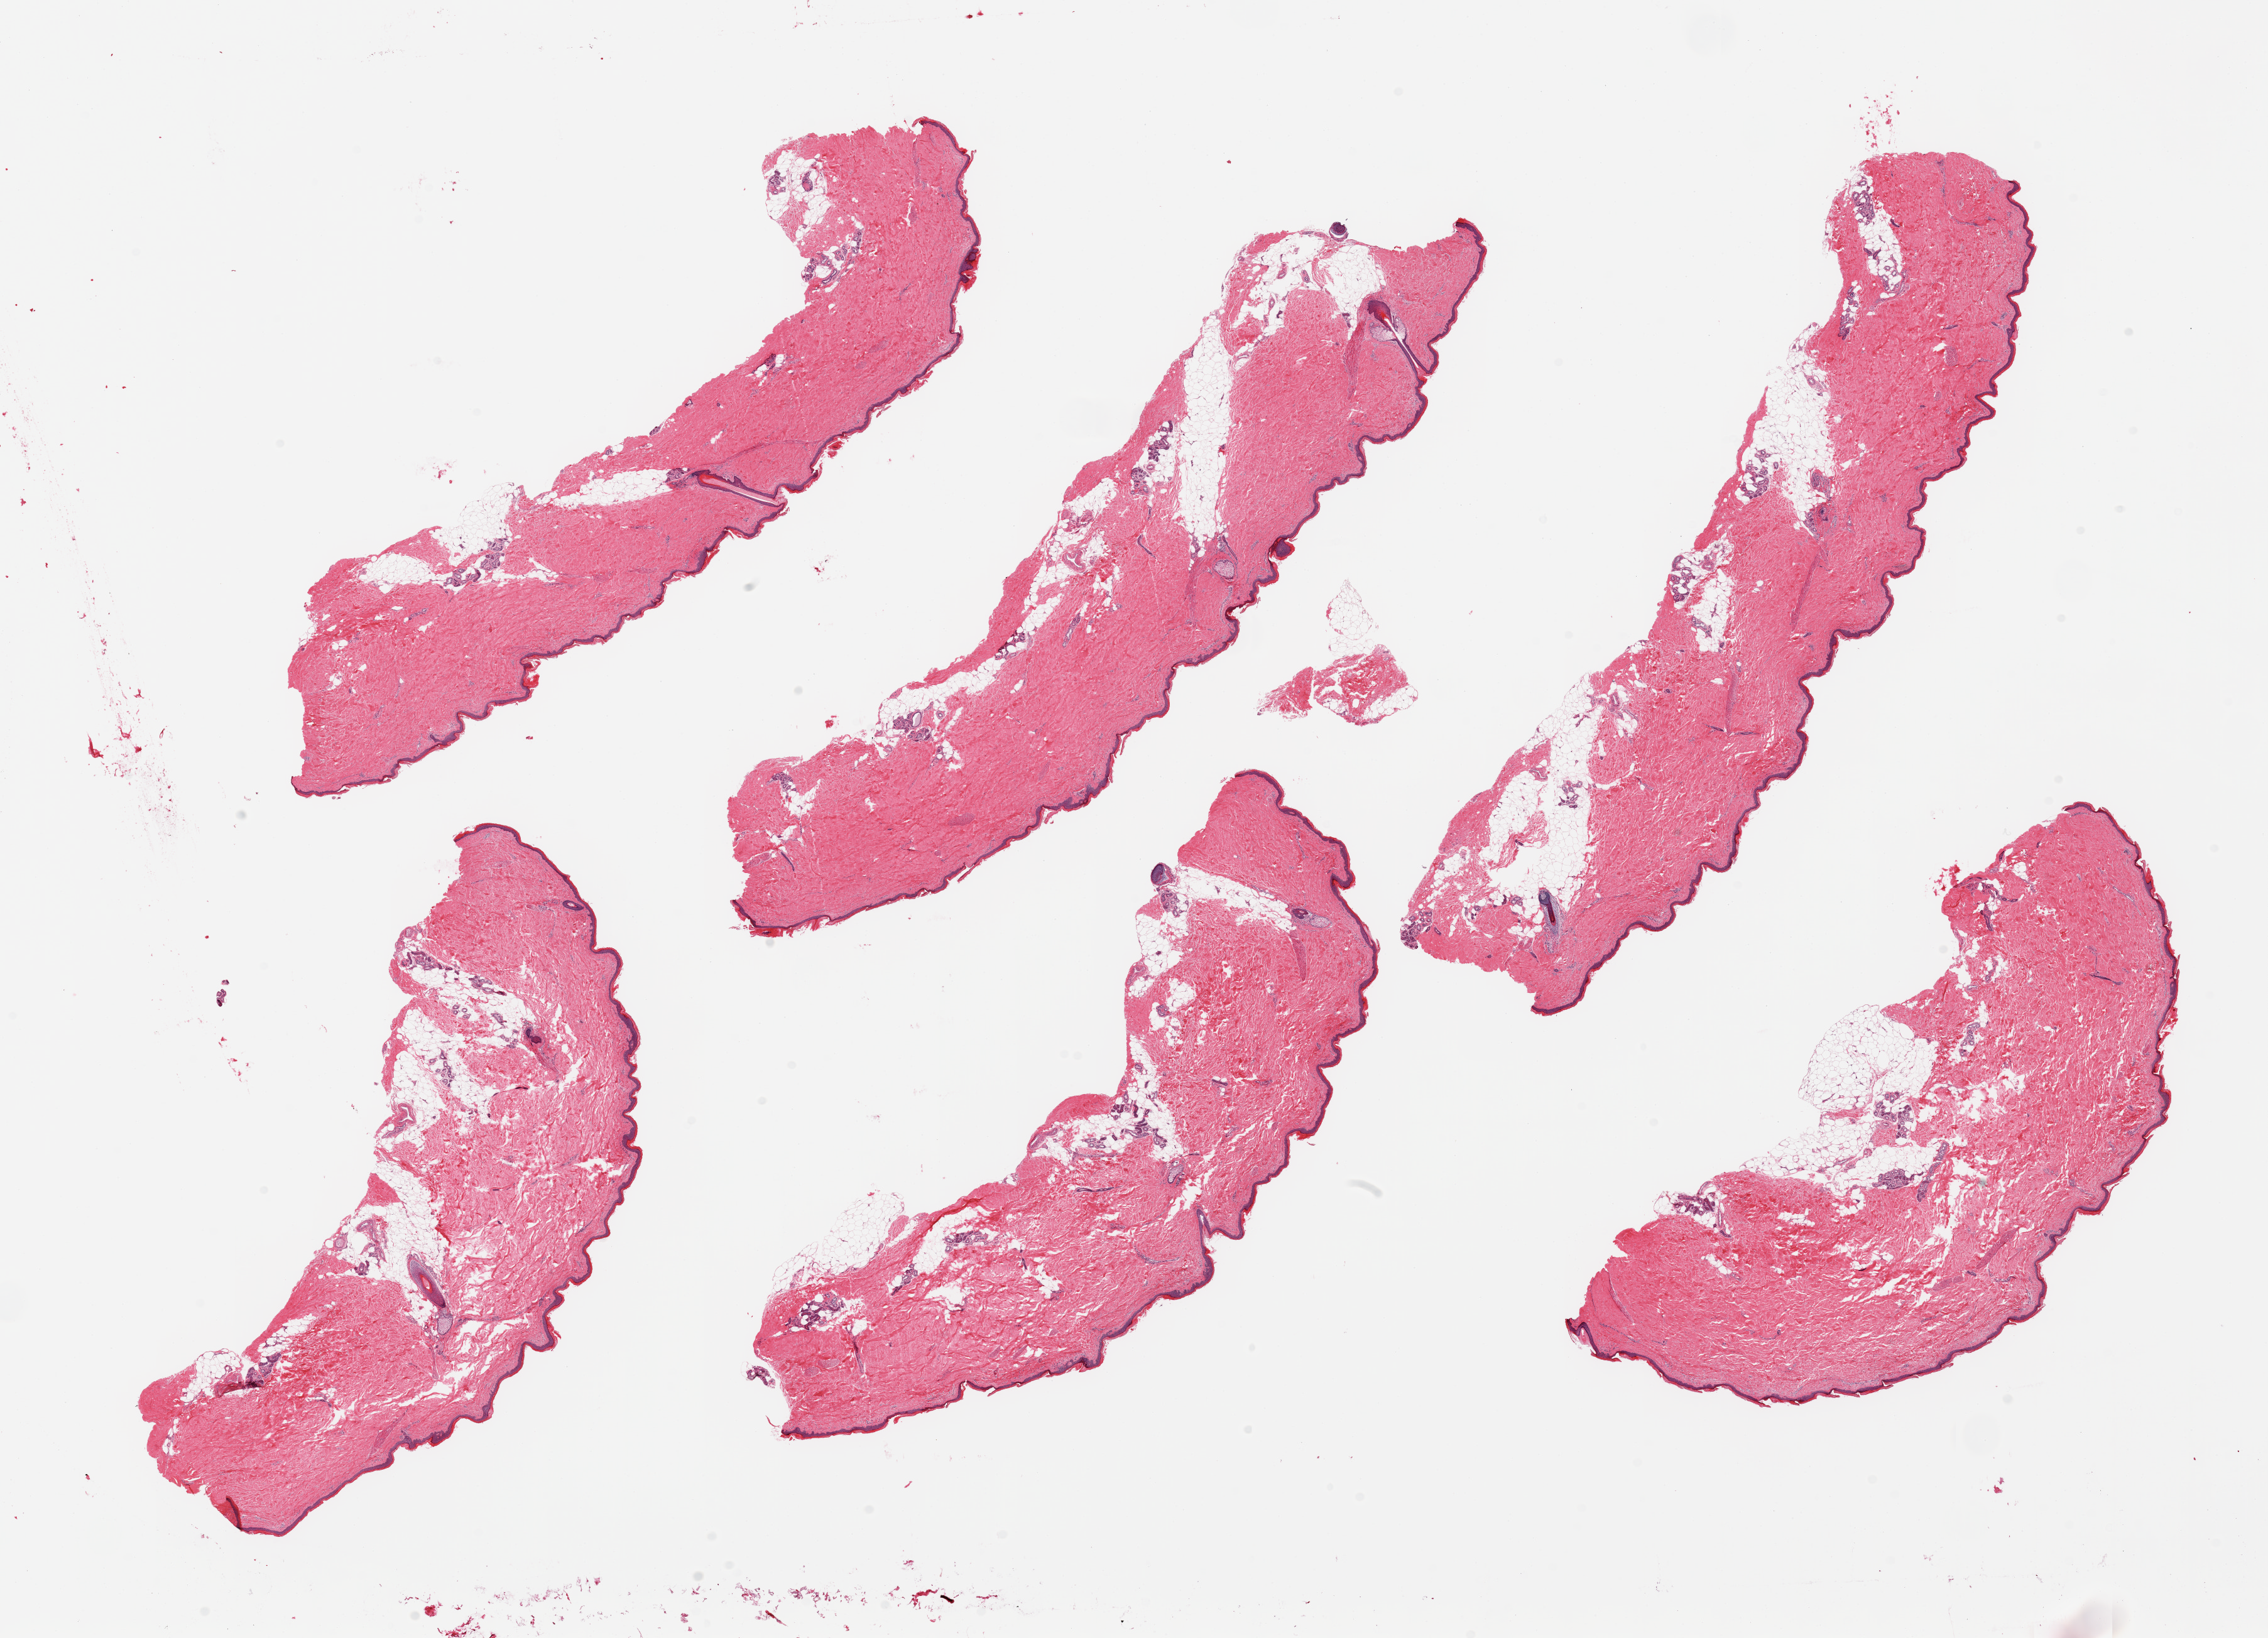
Whole-slide image, H&E stain — whole scanned area (about 28.5 x 20.6 mm) shown as a low-resolution overview, PAXgene-fixed, paraffin-embedded tissue, section of skin of lower leg (target tissue), donor tissue sample. Donor: male.
Reviewer comment on this tissue sample: 6 pieces; 10-20 % intradermal fat.